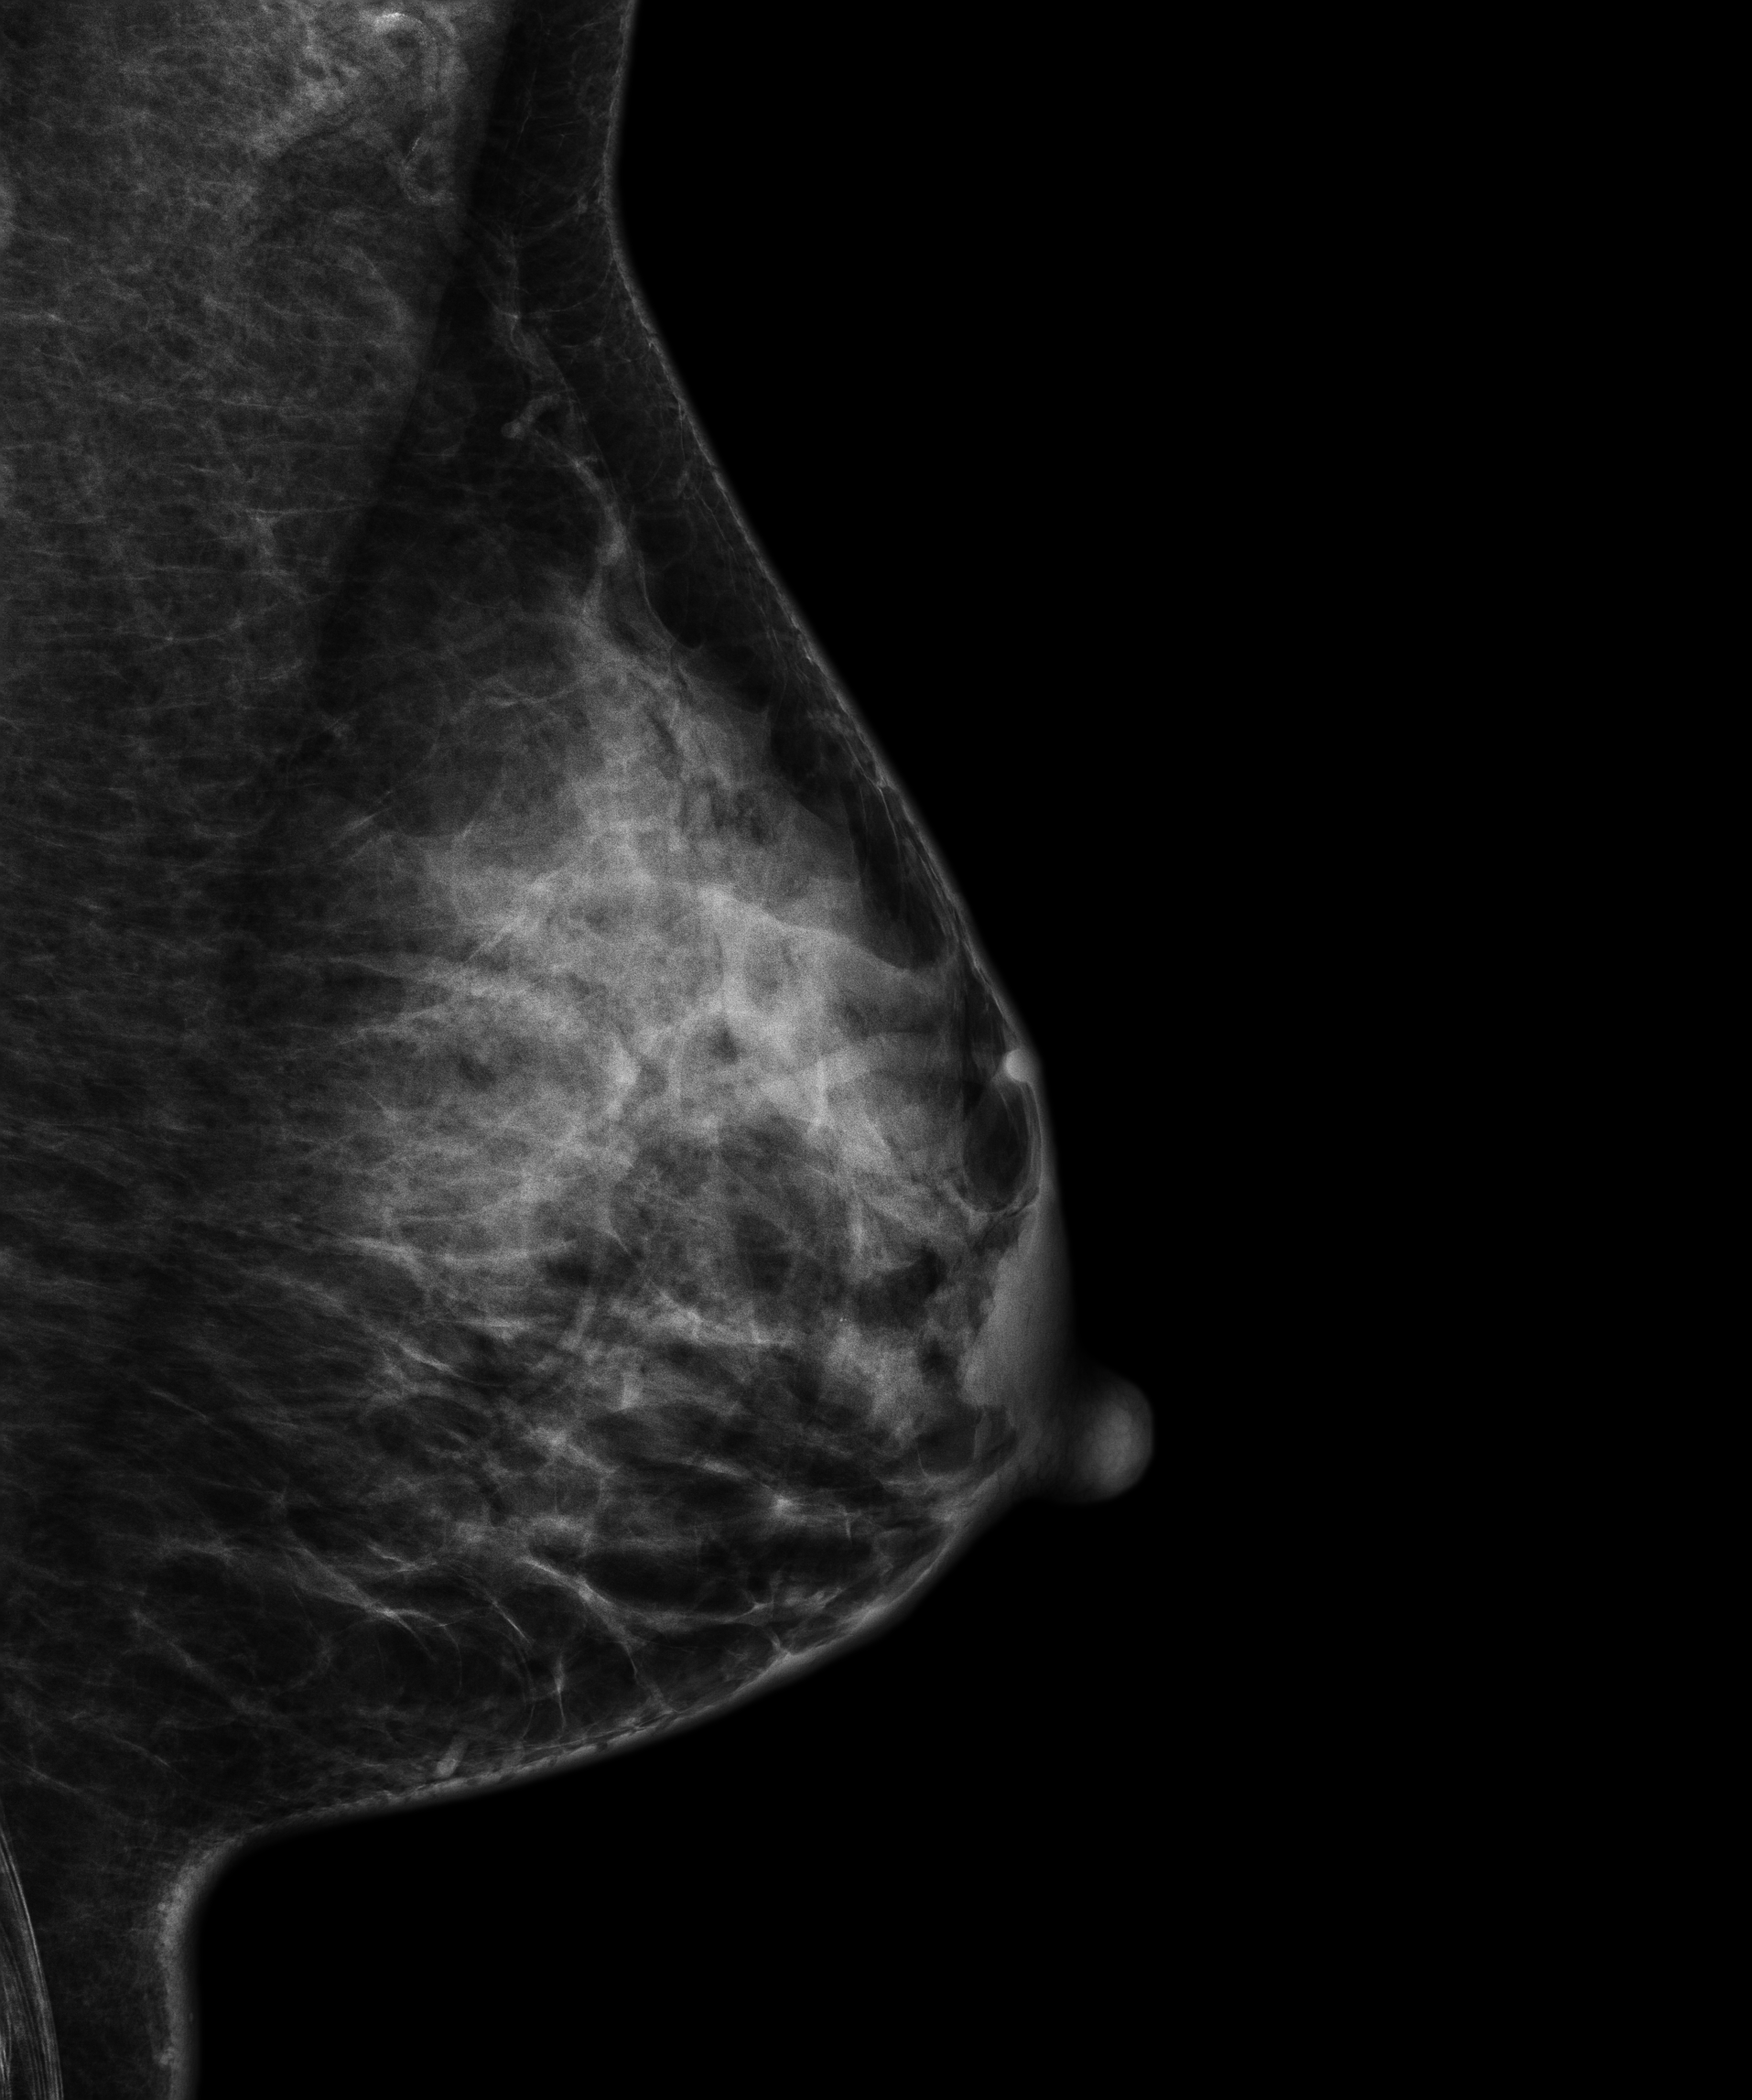
Full-field digital mammogram (FFDM), left breast, mediolateral oblique (MLO) view, screening examination. Patient: female, 55 years.
- breast density at the screening exam (both breasts): heterogeneously dense (BI-RADS density category c)
- final BI-RADS assessment for this screening round (tomosynthesis exam, both breasts): category 1
- recall: no recall after this screen